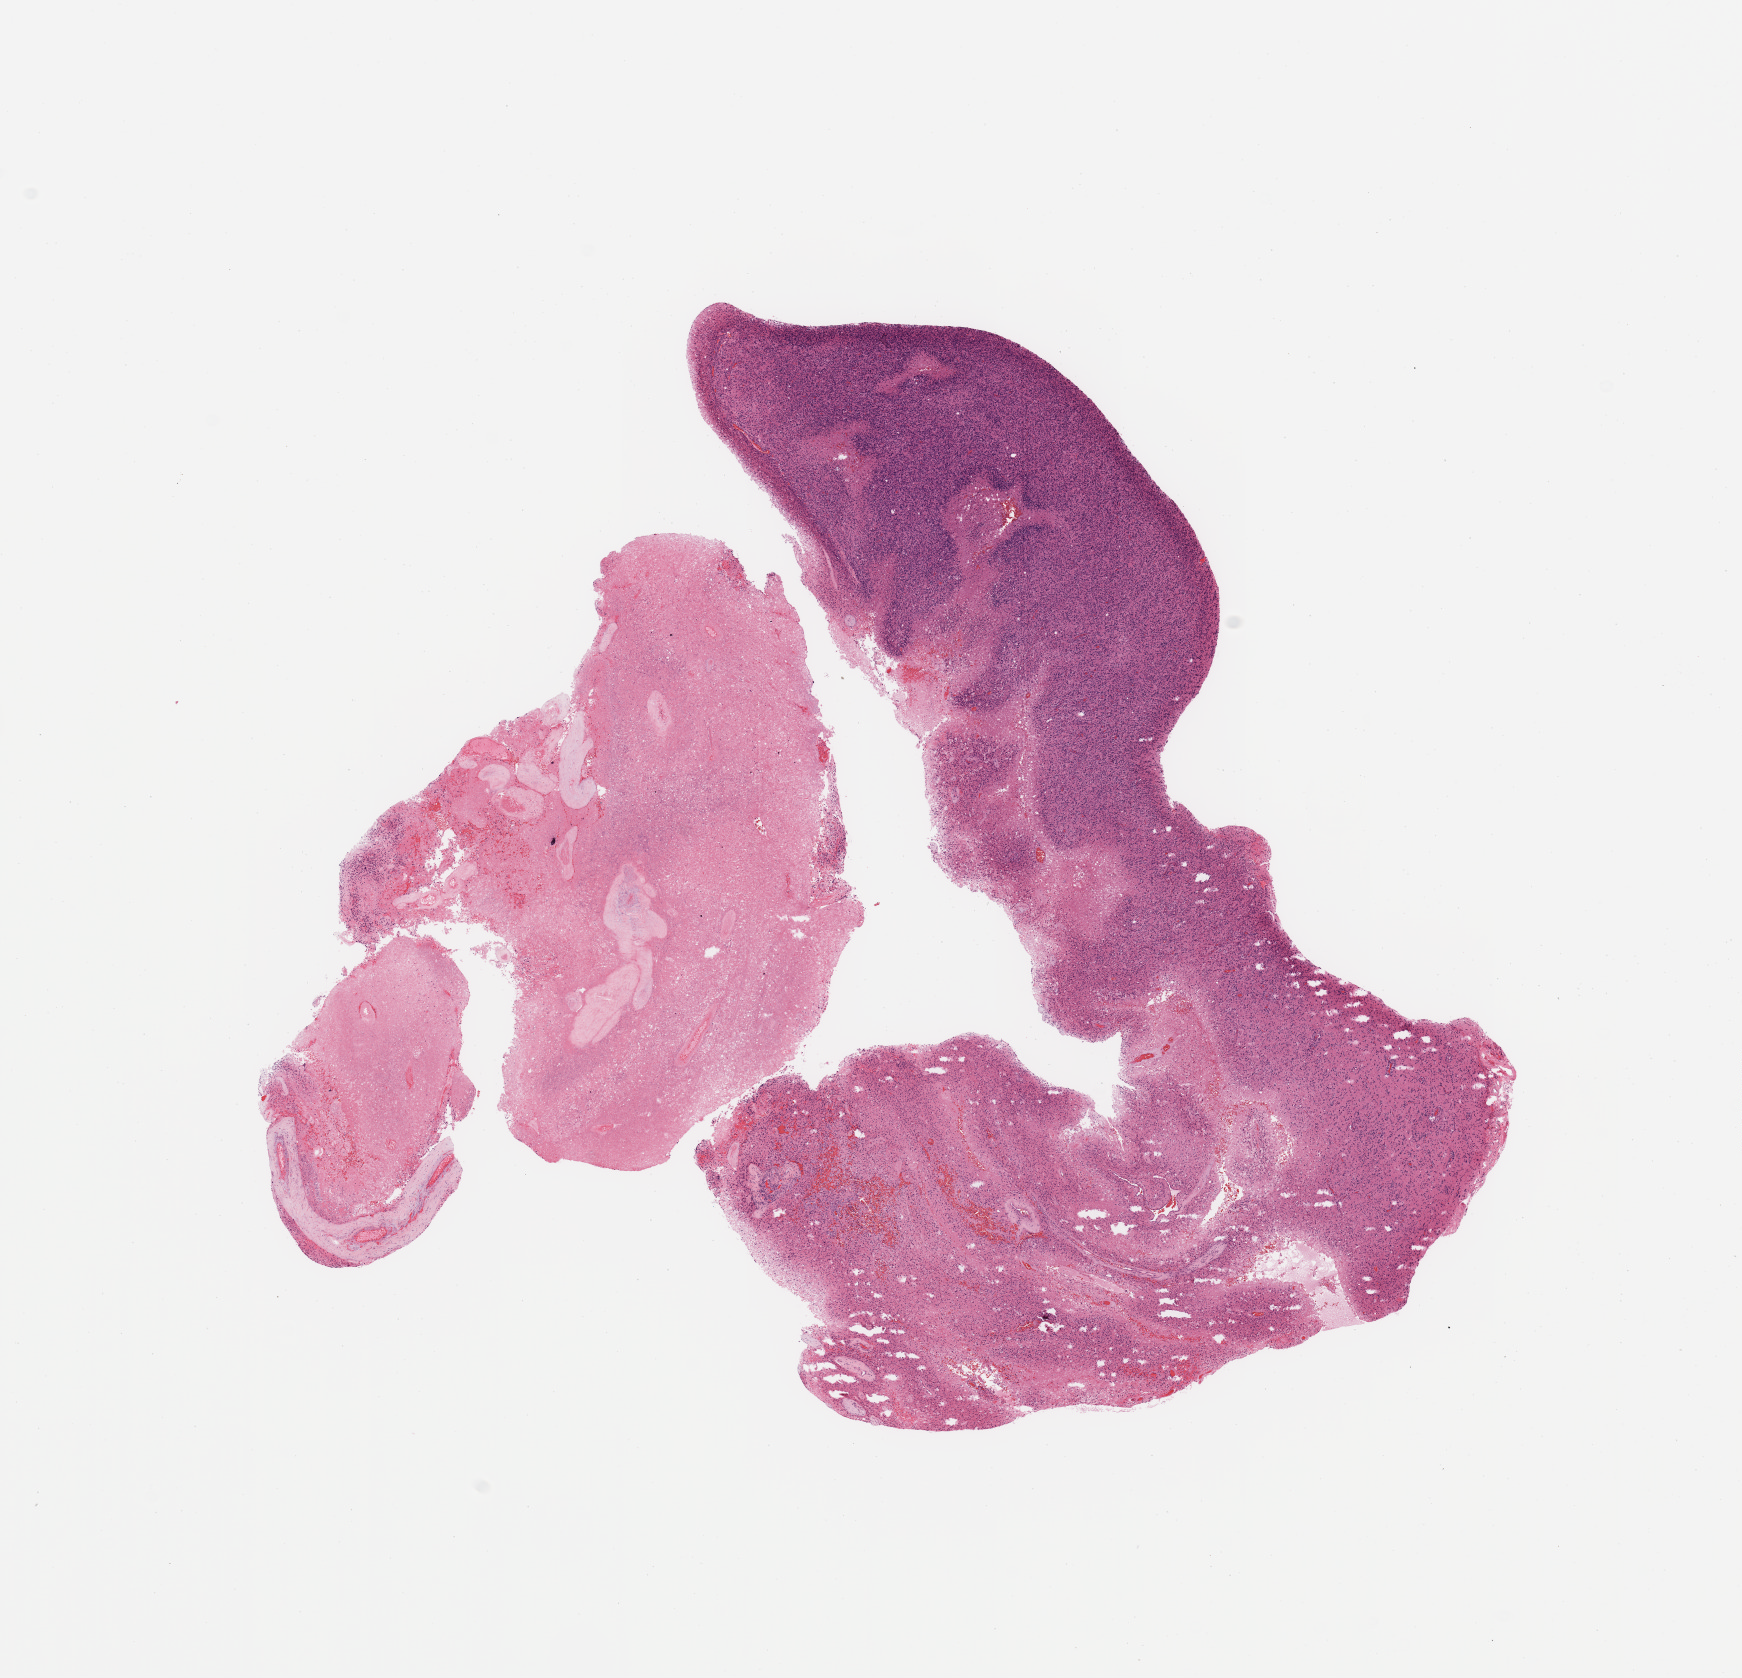
Digitized Hematoxylin and eosin (H&E) stained tissue section (whole slide), whole scanned area (about 13.8 x 13.3 mm) shown as a low-resolution overview; tumour tissue sample, brain. 70-year-old male patient.
Patient diagnosis (cohort enrolment): glioblastoma multiforme (brain).